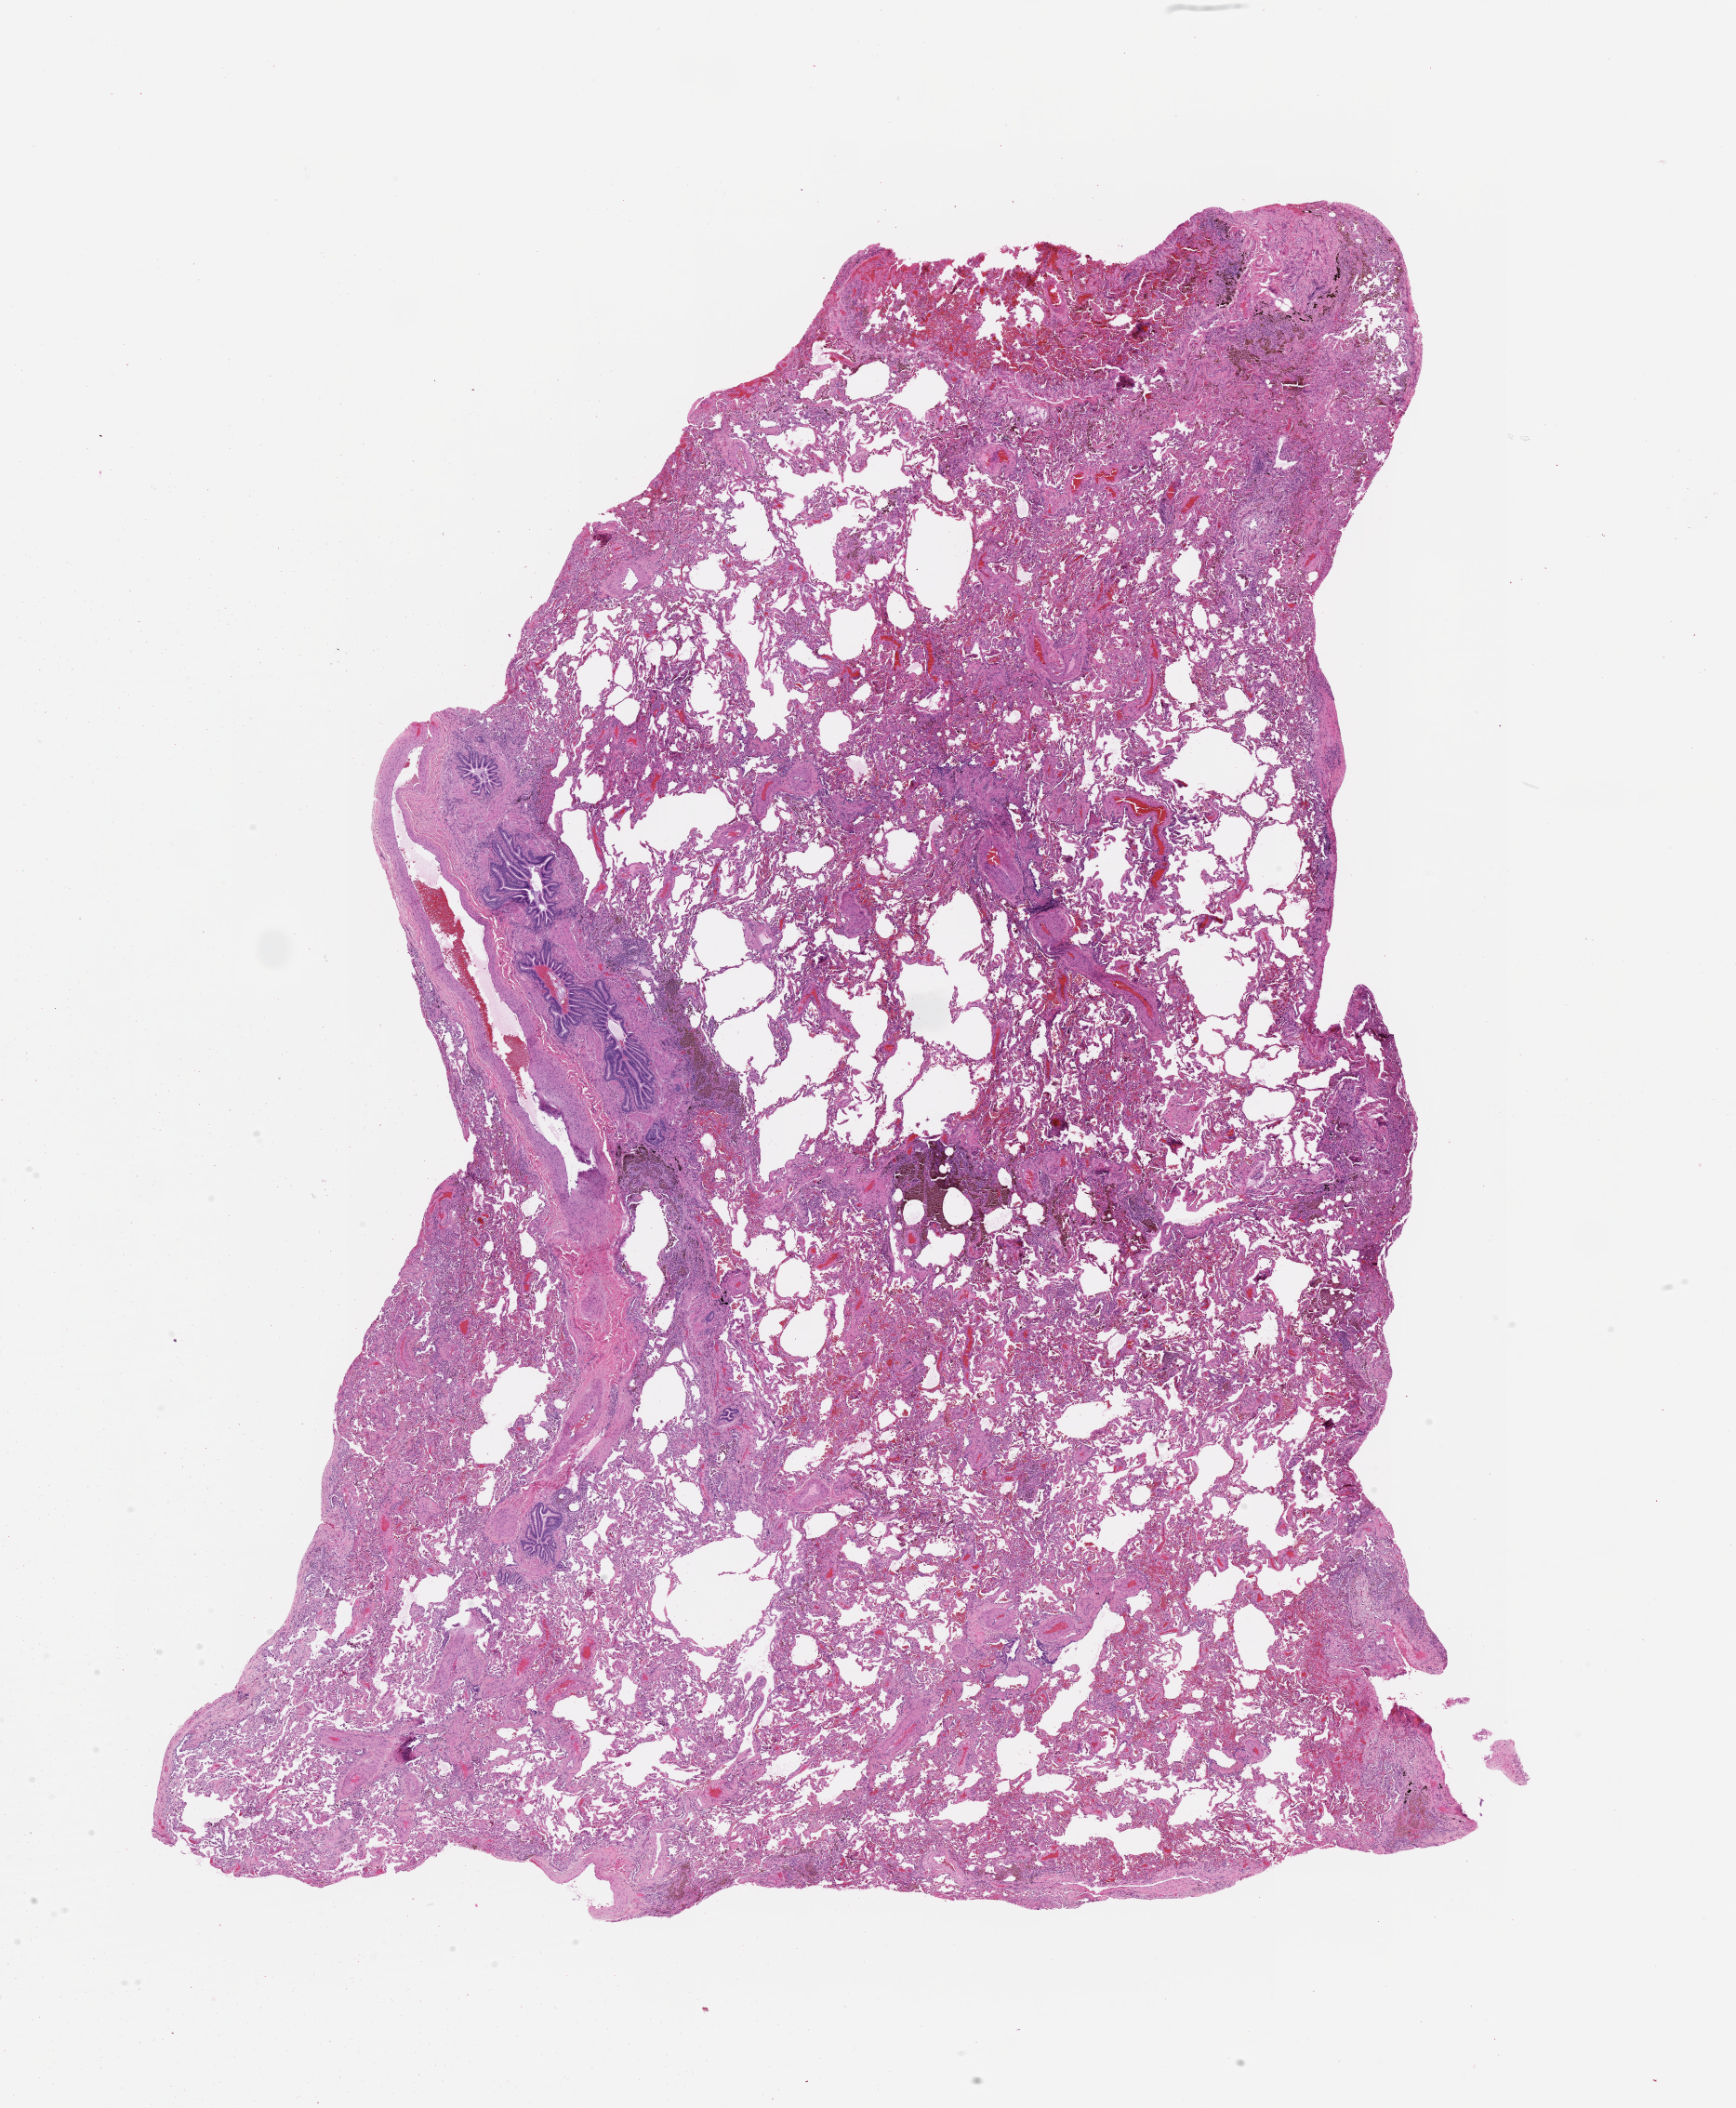
Whole-slide histology image, H&E, shown as a low-resolution overview of the whole scanned area (about 15.0 x 18.3 mm), lung, normal (non-tumour) tissue. 67-year-old male patient.
This section: normal (non-tumour) tissue from the same patient. Patient diagnosis (cohort enrolment): squamous cell carcinoma (lung).